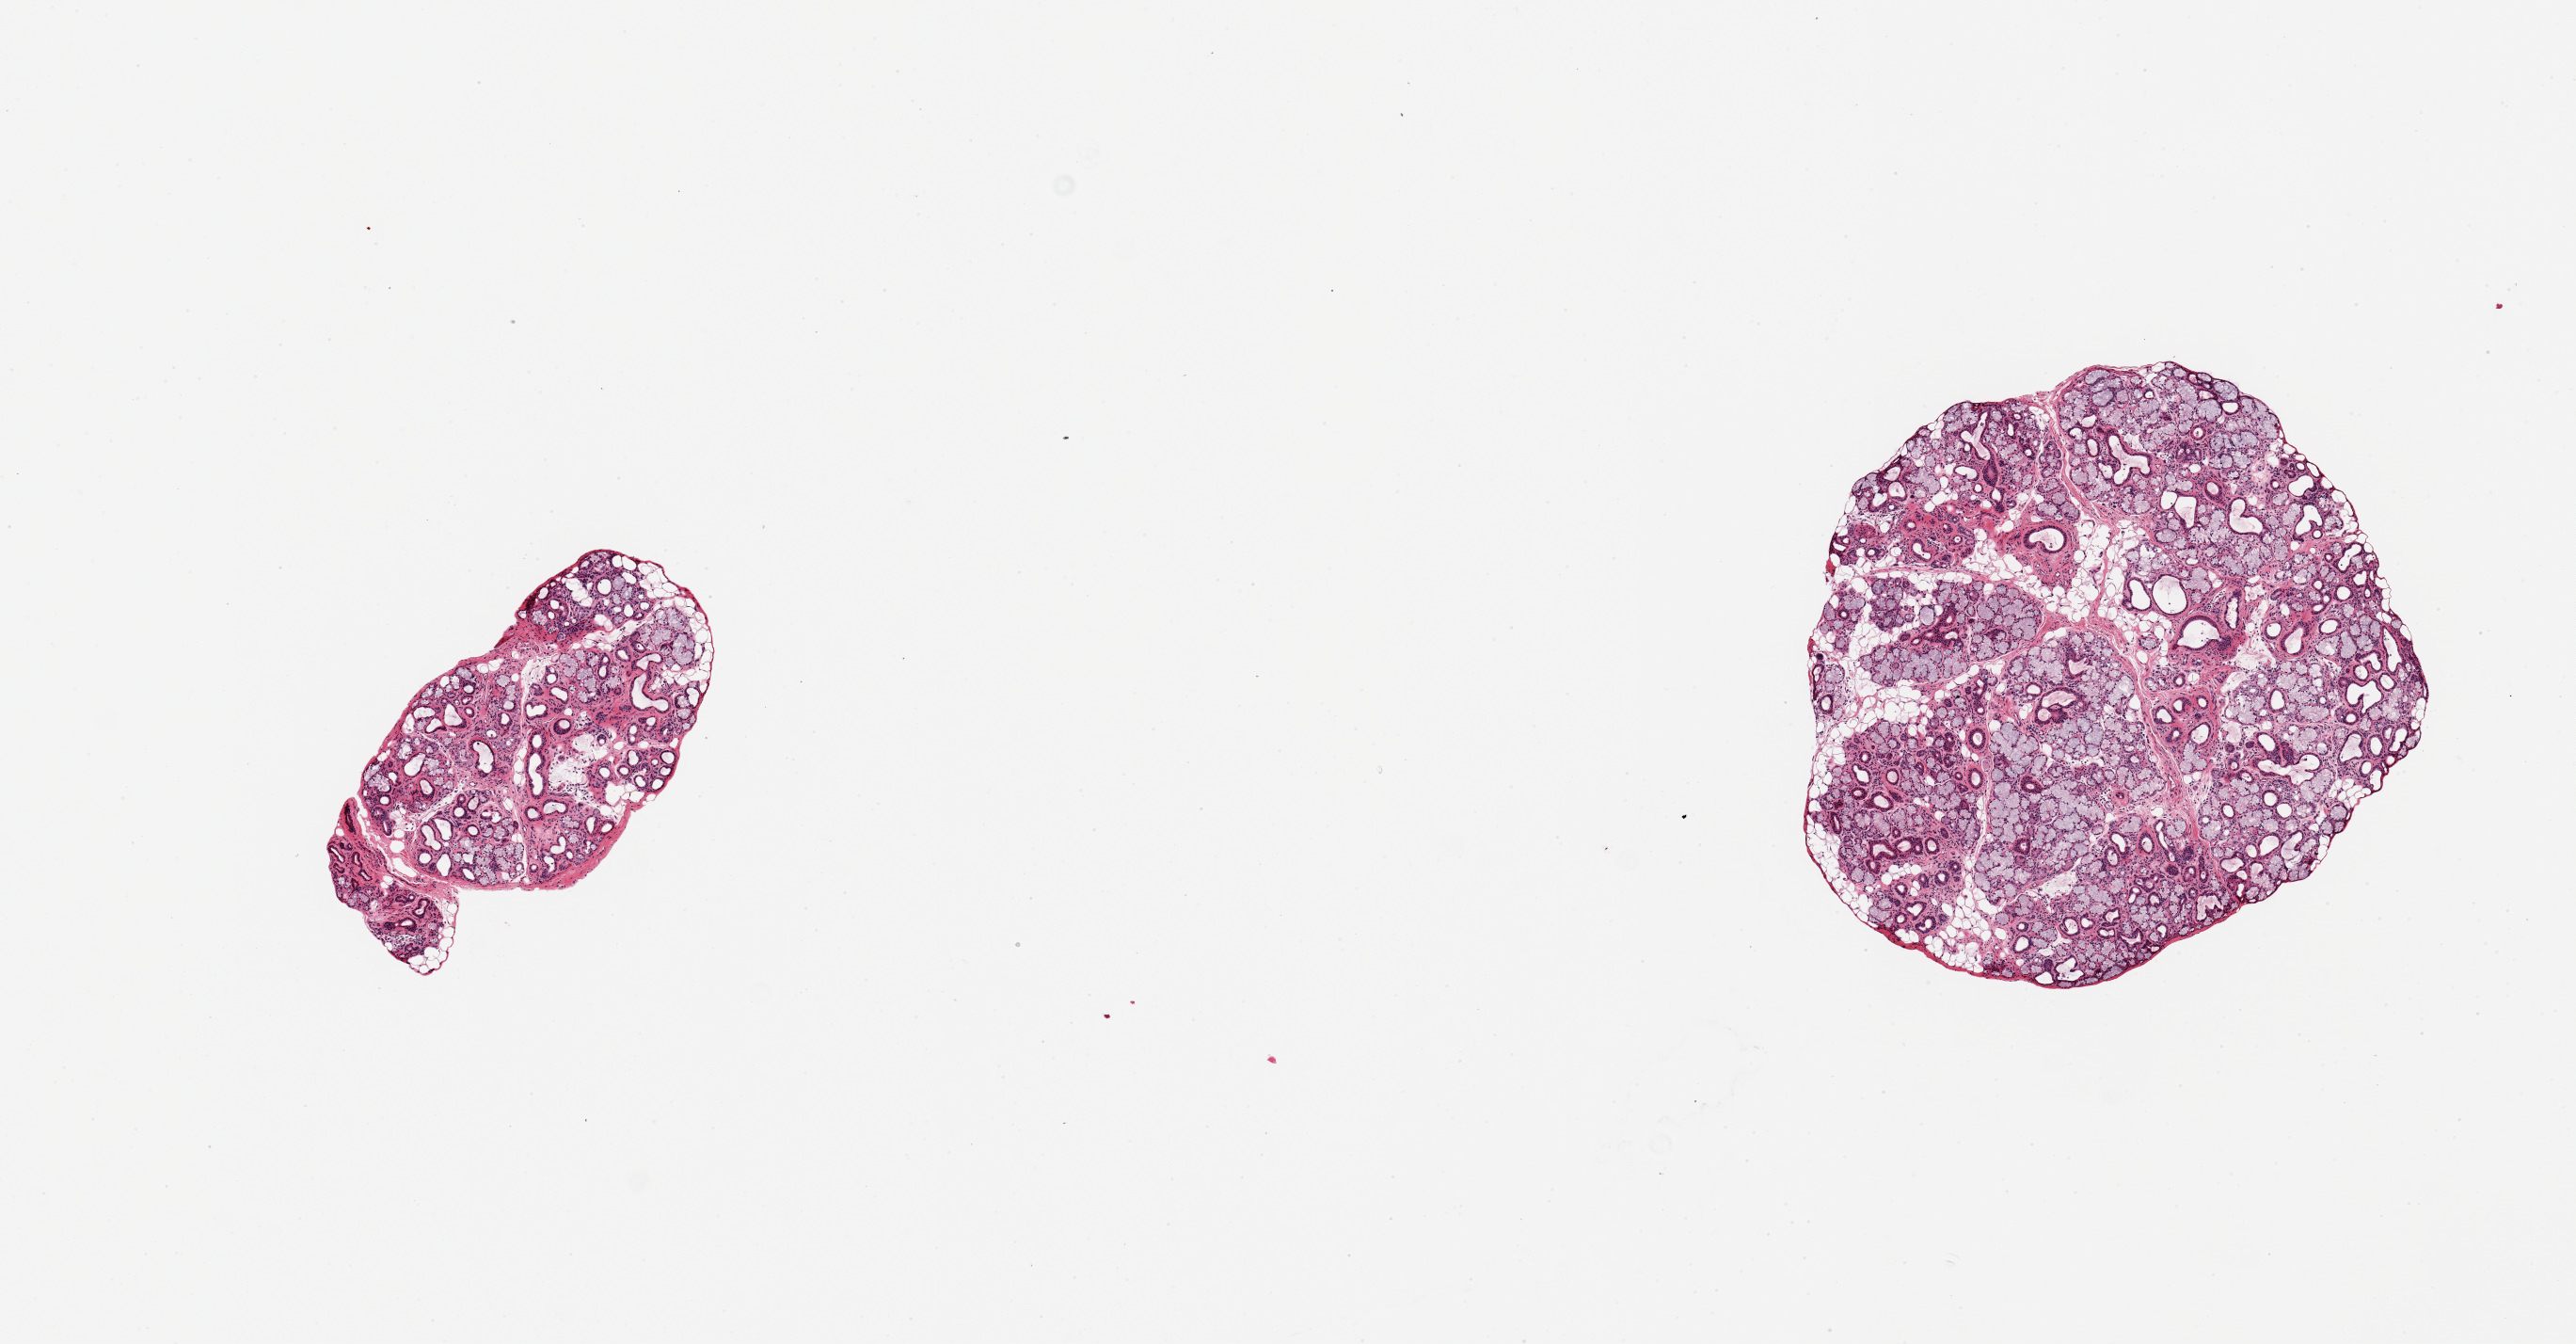
Haematoxylin and eosin whole-slide image, a low-resolution overview of the entire scanned area, about 10.8 x 5.6 mm (slide scanned at 20x). PAXgene-fixed paraffin-embedded (PFPE) section. Sampled site (target tissue): minor salivary gland. Donor tissue sample. Female donor.
• review note (as recorded): 2 pieces; well dissected glands; moderate ductal dilatation, atrophy and fibrosis